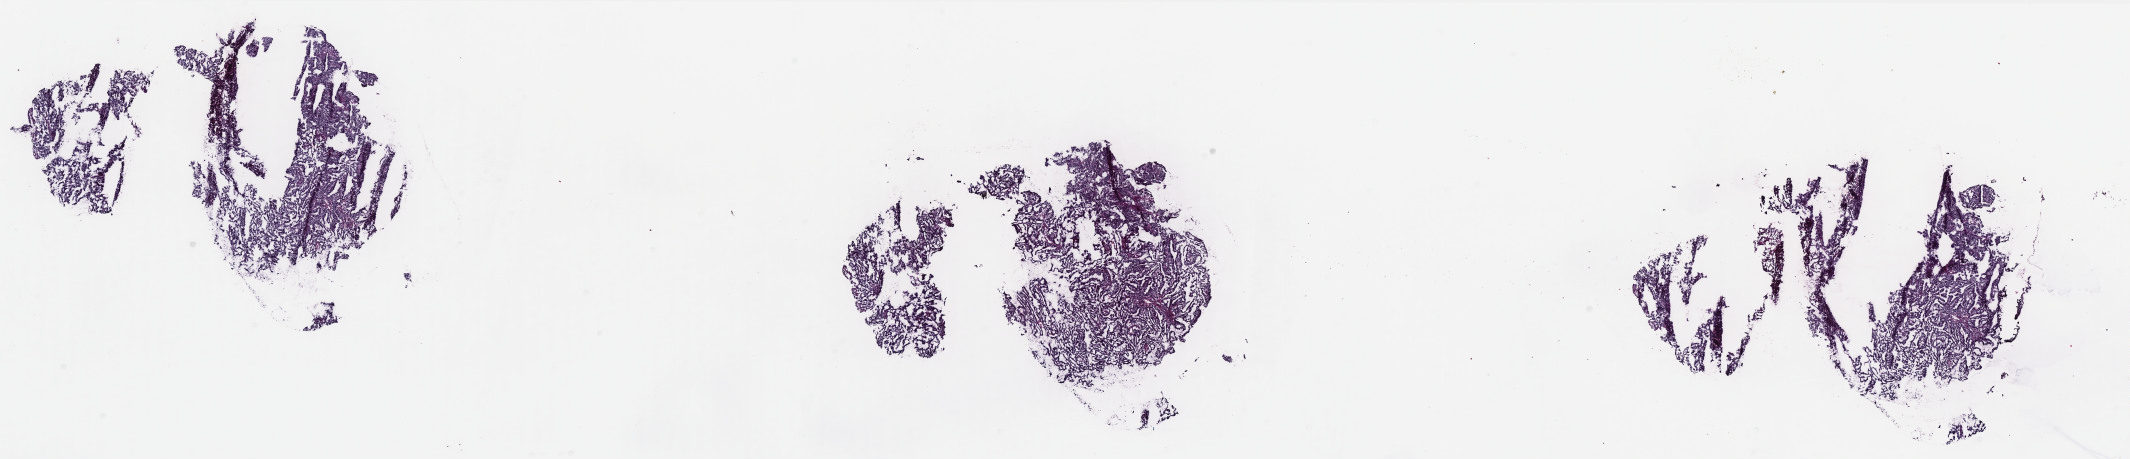
H&E whole-slide image — a low-resolution overview of the entire scanned area, about 34.2 x 7.4 mm (slide scanned at 40x); frozen section; uterus, primary tumour sample. Patient: female, age at initial diagnosis 63 years. Histologic grade: G2 (moderately differentiated). Pathologist review of this section (percent, as recorded): tumour cells 100%, tumour nuclei 90%, normal cells 0%, stromal cells 0%, necrosis 0%. Infiltration values recorded for this section: lymphocyte infiltration 1%, monocyte infiltration 0%, neutrophil infiltration 0%.
- lymph nodes positive (case pathology): 0 of 6 examined
- FIGO stage: IA
- diagnosis: Endometrioid adenocarcinoma, NOS (endometrium)